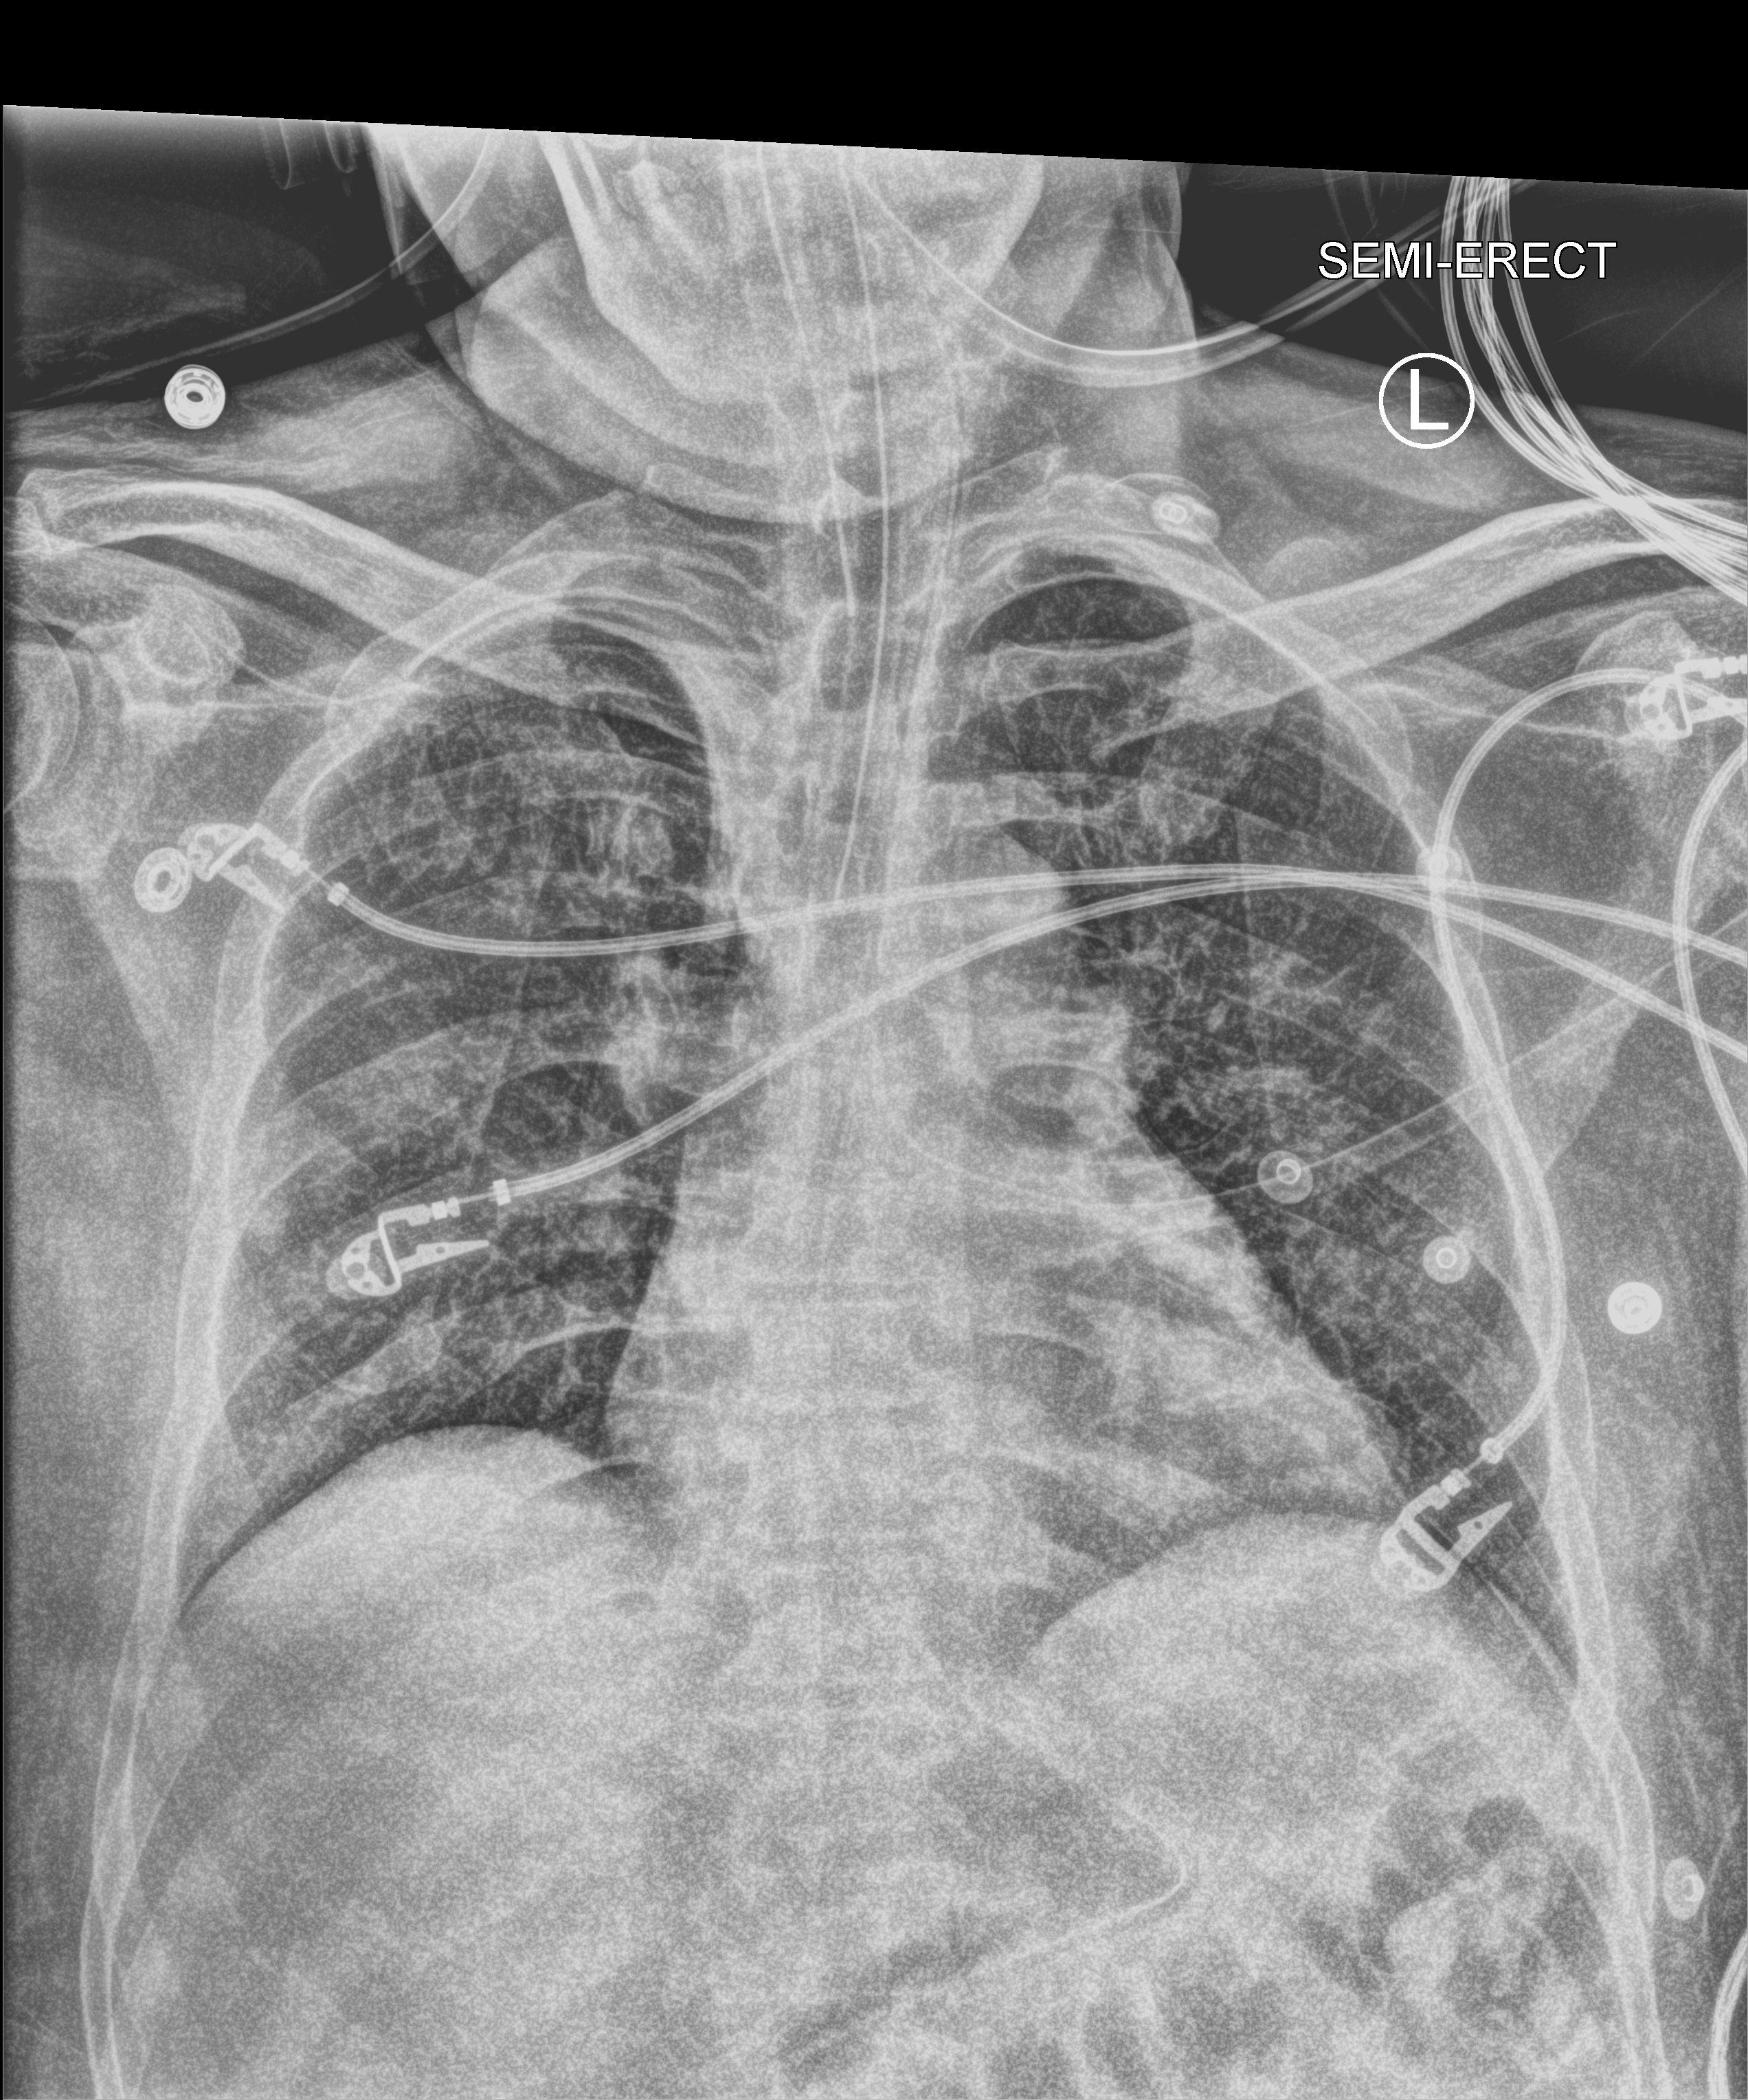
Chest X-ray (portable). Patient hospitalised with COVID-19, aged 18–59 years.
Admission-level facts for this patient (not findings on this image; timing relative to this image not recorded): length of hospital stay: 37 days; mechanically ventilated during this hospital stay: yes; admitted to intensive care during this hospital stay: yes.